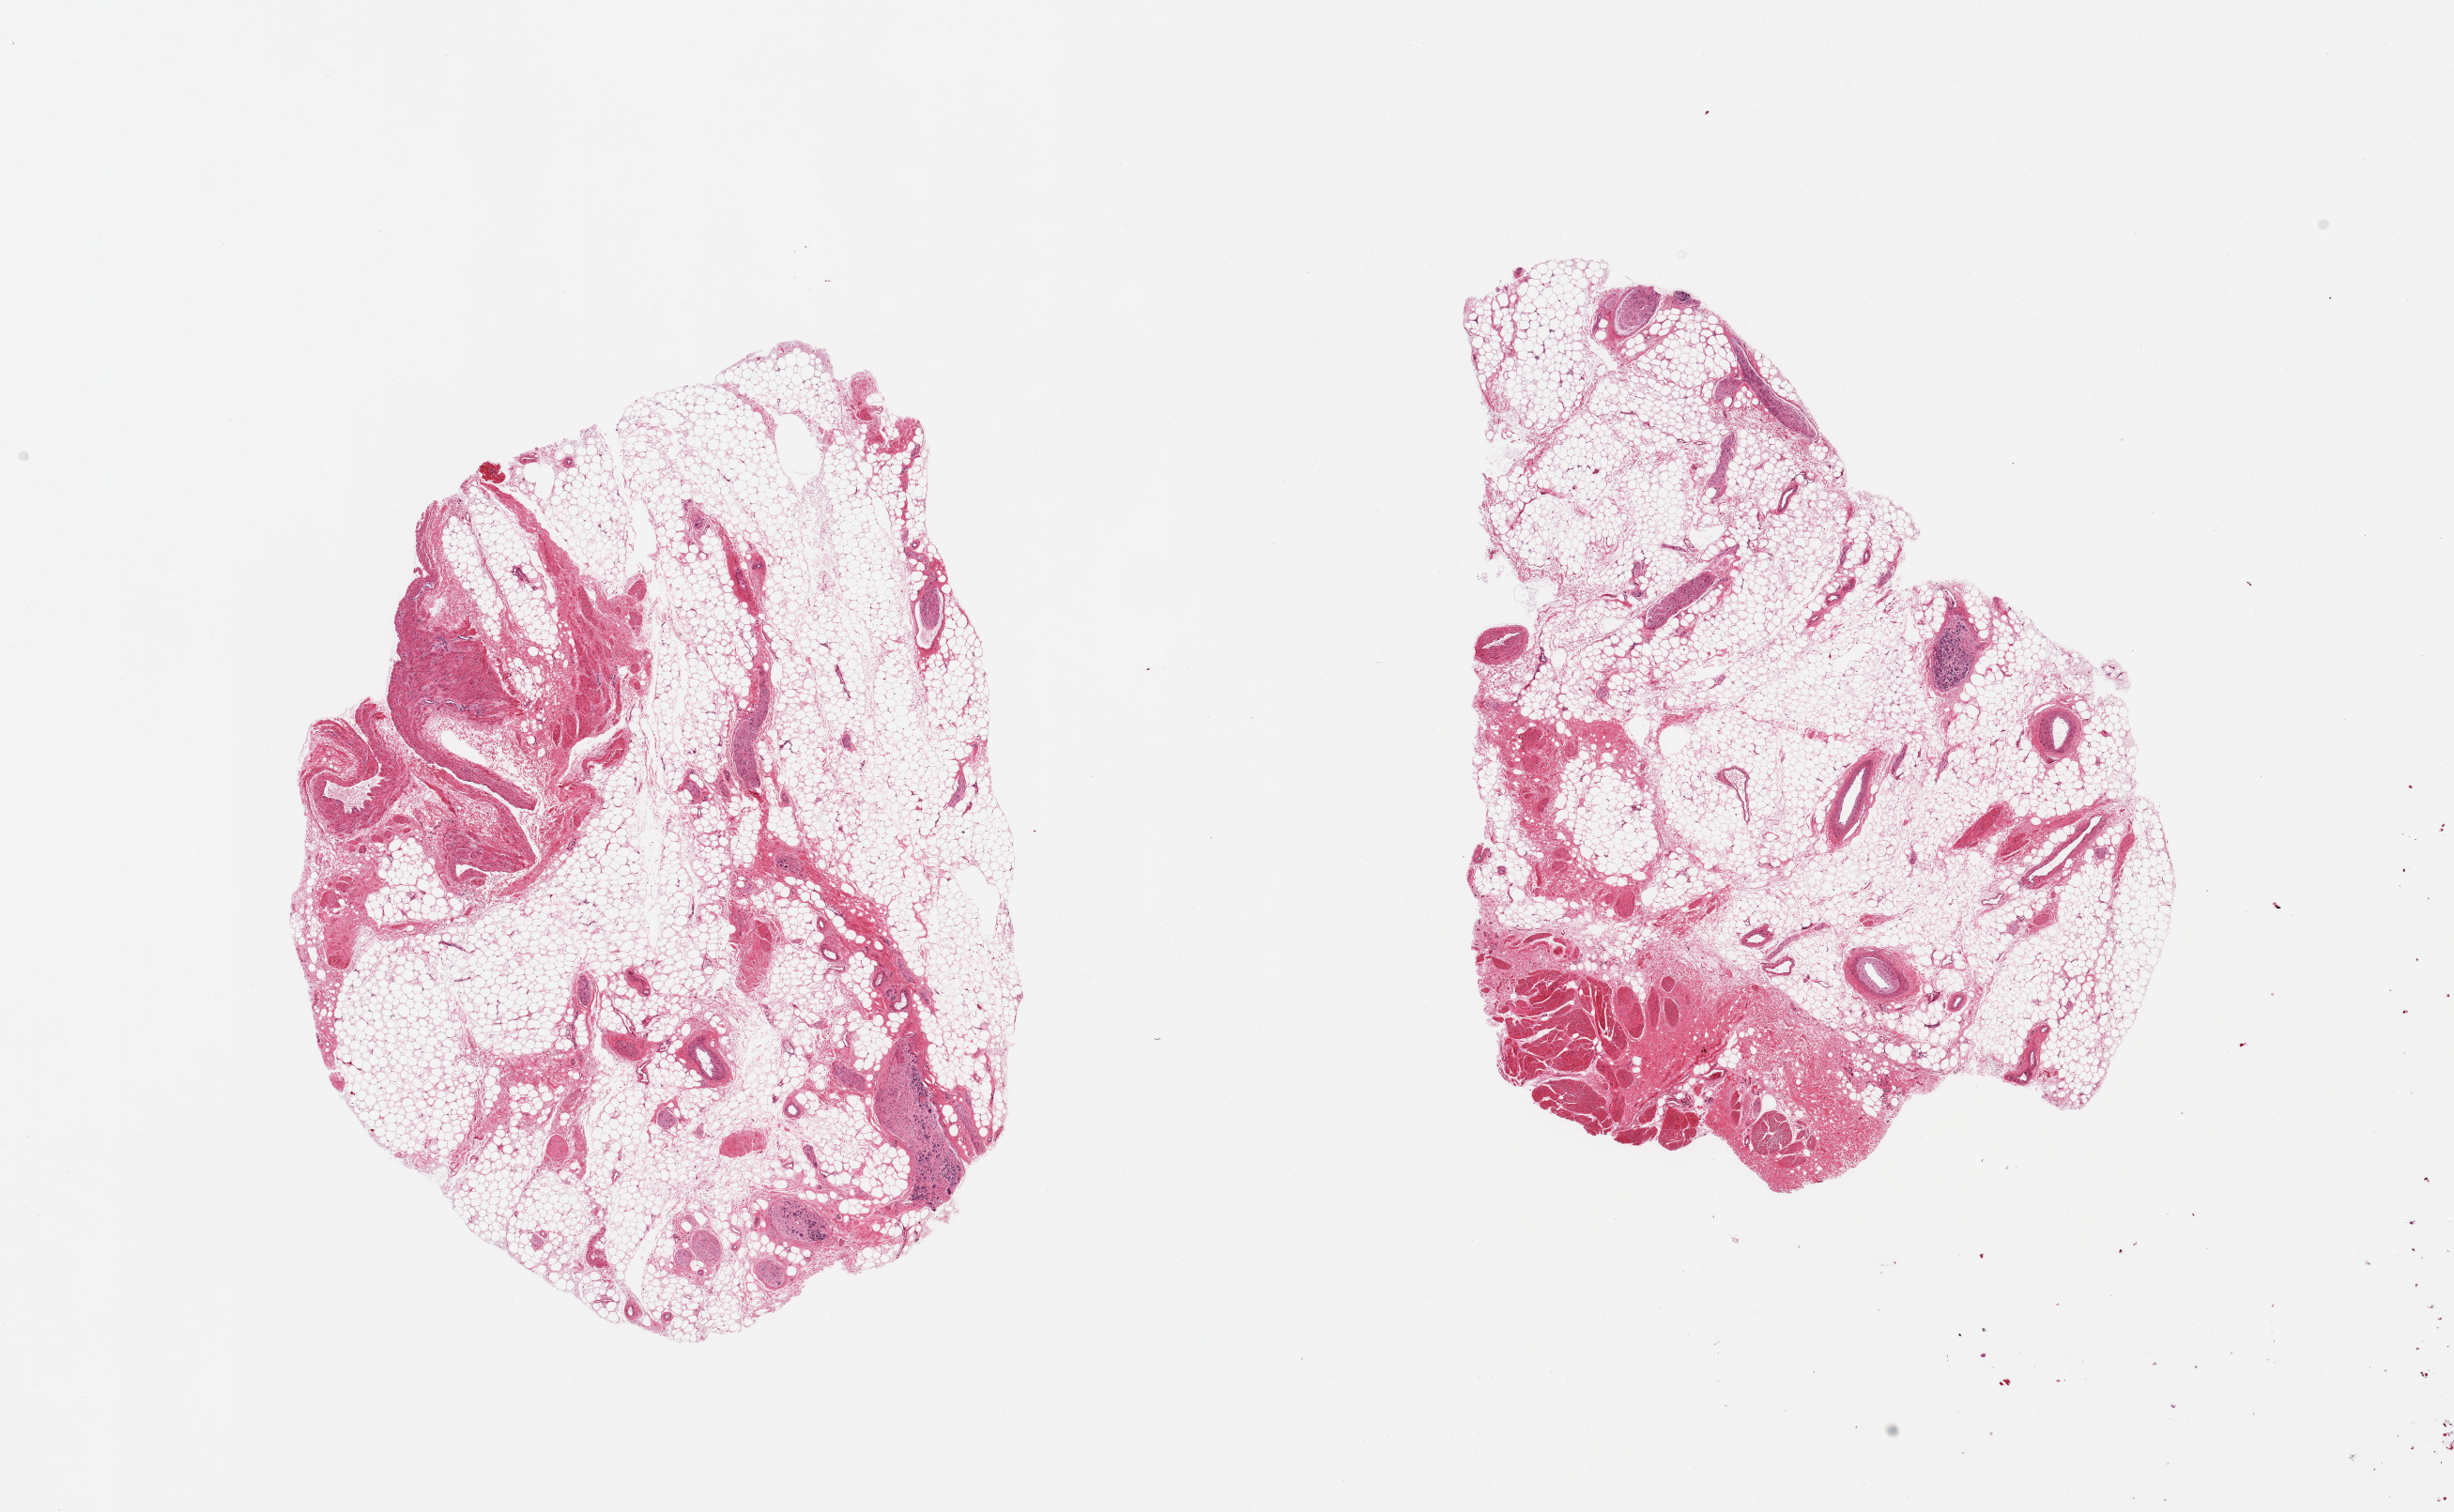
Whole-slide image, hematoxylin and eosin (H&E) stain, brightfield, low-resolution overview of the scanned area, about 20.7 x 12.7 mm; PAXgene-fixed paraffin-embedded (PFPE) section; target tissue: prostate; tissue donor sample. Donor sex: male.
Pathologist's review note for this sample: 2 pieces; mostly adipose tissue with fibrovascular component, nerves and gangions; focal fibromuscular tissue; no target tissue present.